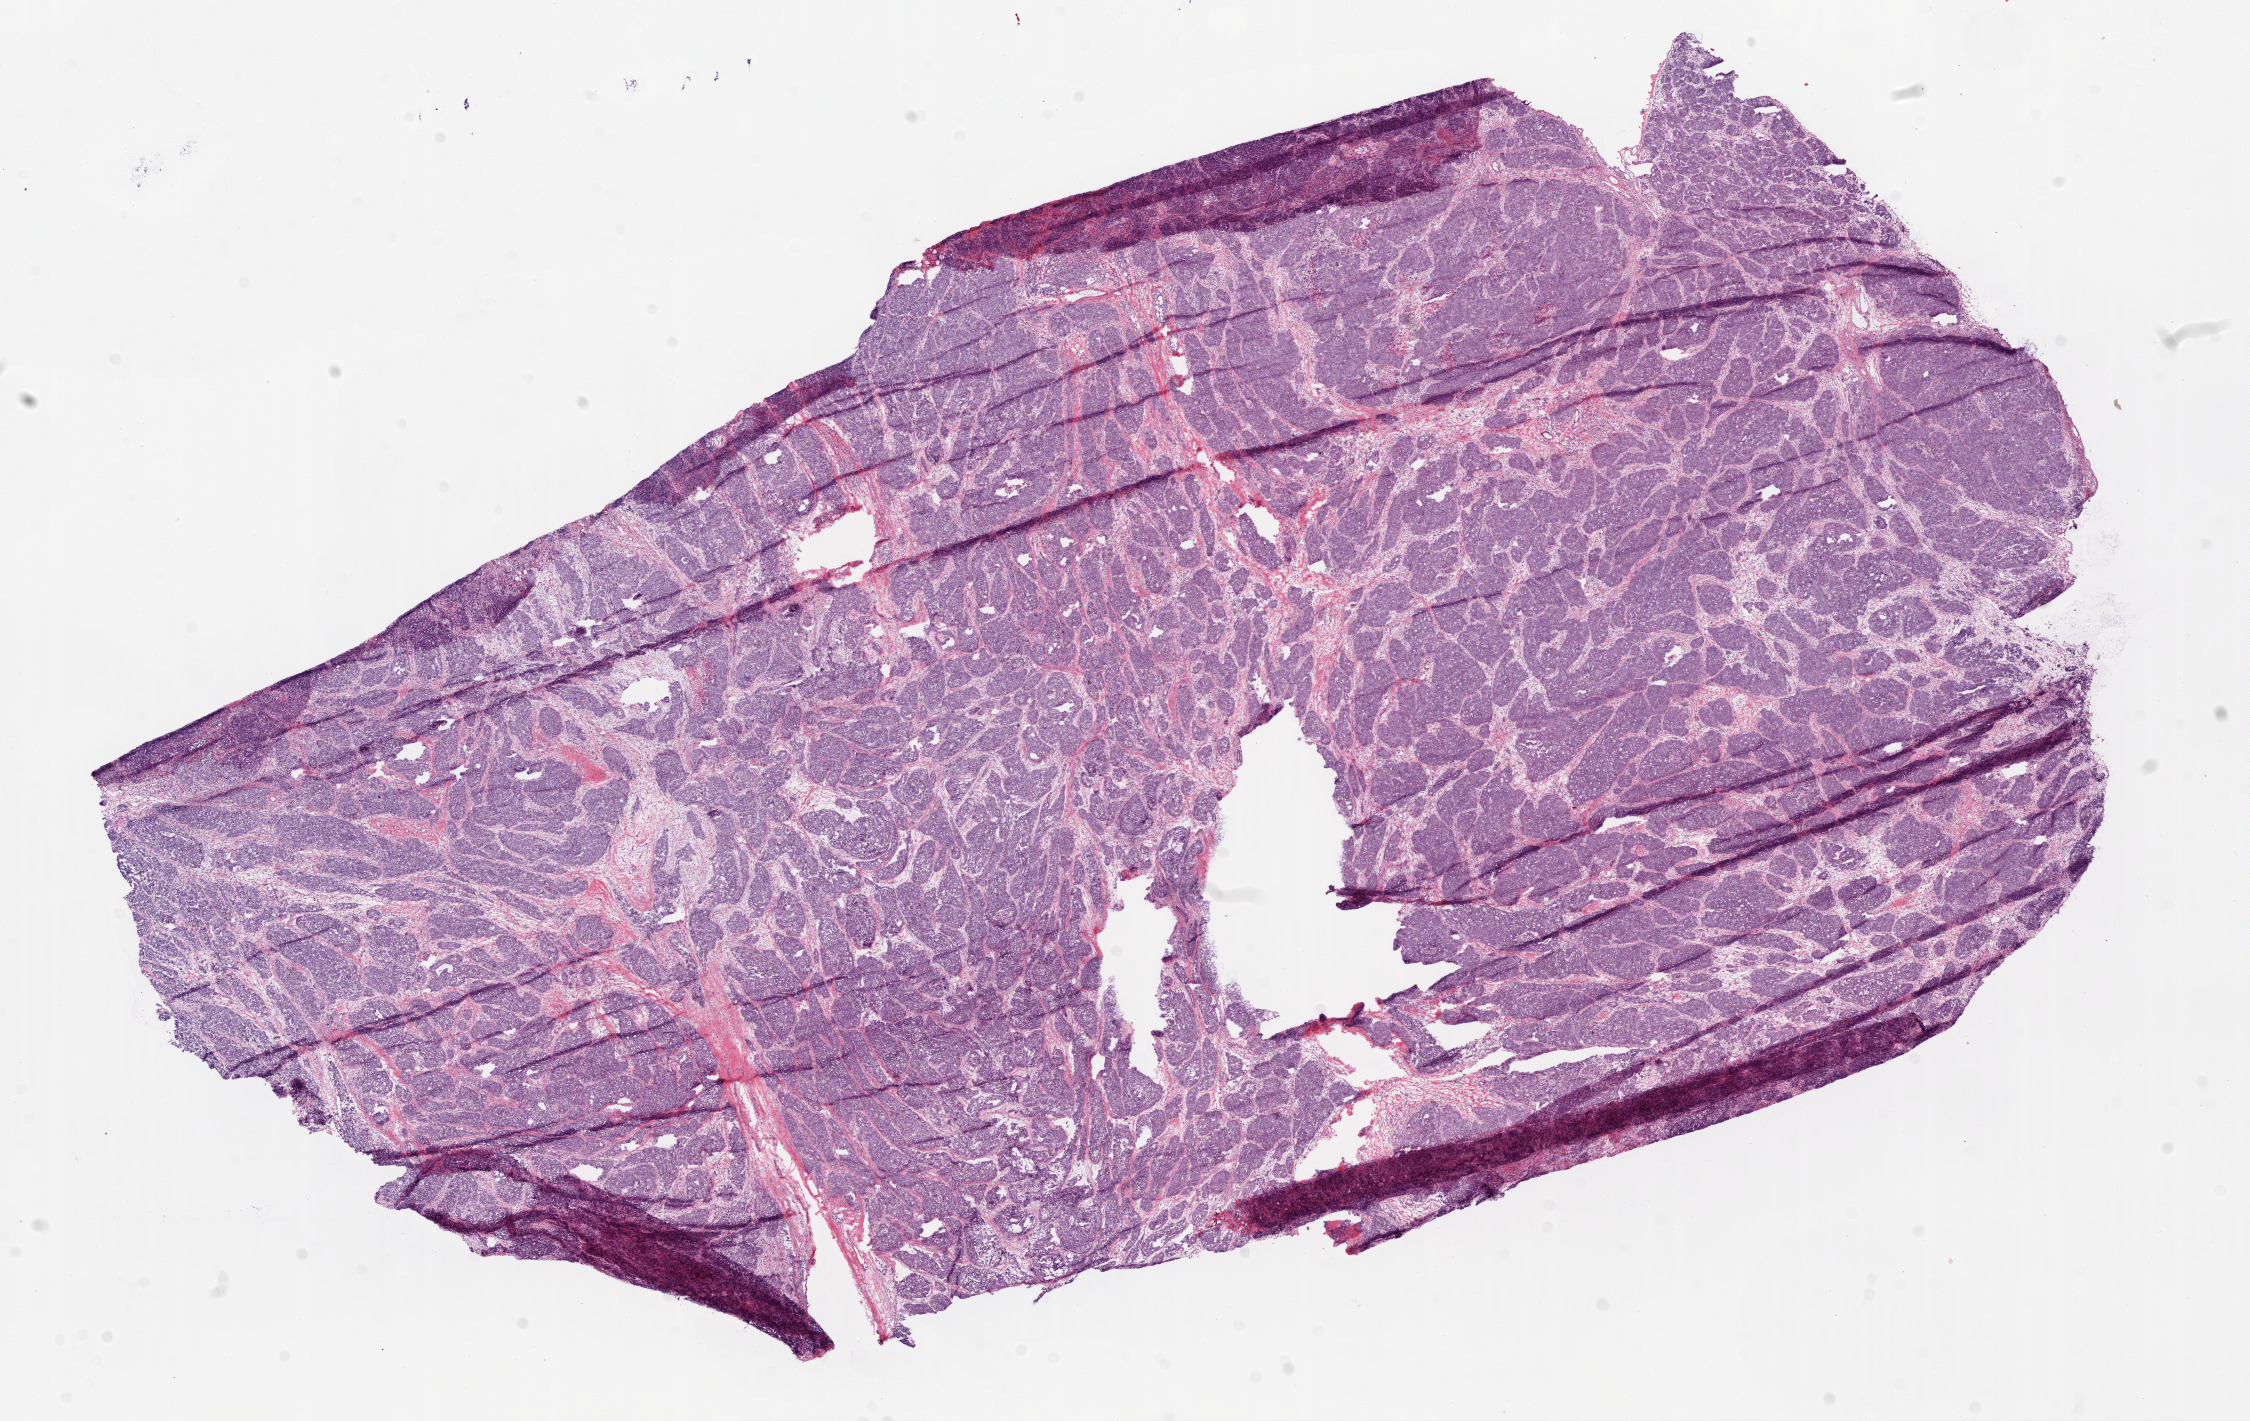
Digitized H&E tissue section (whole slide), whole scanned area (about 18.1 x 11.4 mm, slide scanned at 20x) shown as a low-resolution overview, frozen section, sample: primary tumour, ovary. Patient: female, age at initial diagnosis 76 years. Histologic grade: G3 (poorly differentiated). Pathologist review of this section (percent, as recorded): tumour cells 85%, tumour nuclei 90%, normal cells 1%, stromal cells 9%, necrosis 5%.
FIGO stage: IIIC. Histologic diagnosis: Serous cystadenocarcinoma, NOS.